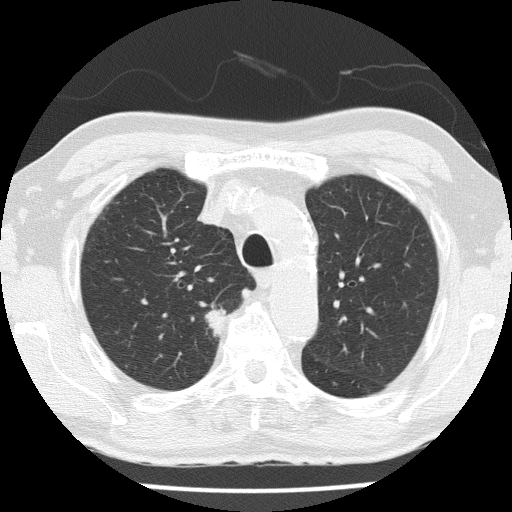
Low-dose screening chest CT, one axial slice; slice 111 of 153 in the series (ordered by position); reconstruction kernel FC51; lung window (W 1500 / L -600 HU); 2 mm slice thickness; 512 × 512 image matrix, field of view 323 × 323 mm.
Structures marked on this image (outlined manually by an expert reader):
- lesion 1 (tumor, upper lobe of right lung): bounding box [x1, y1, x2, y2] px = [206, 305, 225, 336]